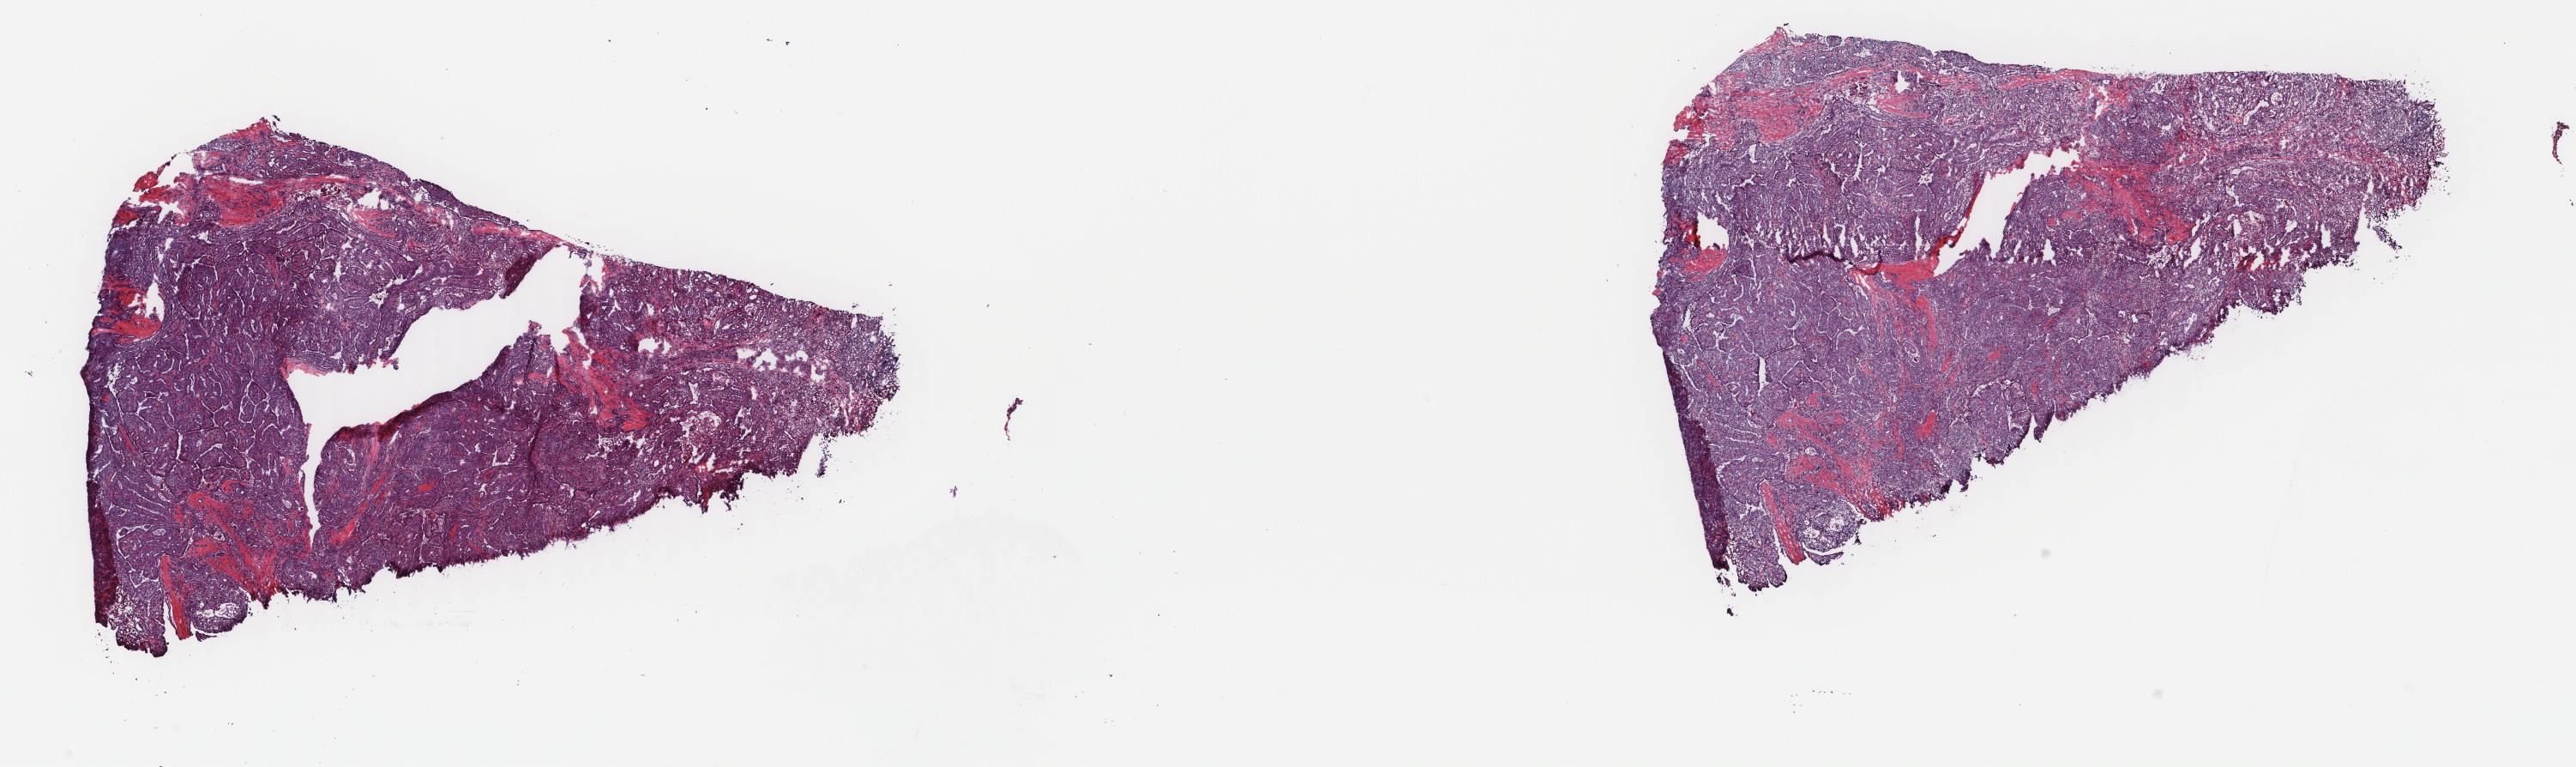
Digitized H&E-stained tissue section (whole slide), whole scanned area (about 23.8 x 7.1 mm) shown as a low-resolution overview, frozen section from the top of the tissue portion, primary tumour sample from the thyroid. Female, age 21 years at initial diagnosis. Pathologist review of this section (percent, as recorded): tumour cells 85%, tumour nuclei 65%, normal cells 5%, stromal cells 10%, necrosis 0%. Inflammatory infiltration, as recorded: lymphocyte infiltration 0%, monocyte infiltration 0%, neutrophil infiltration 0%.
Histologic diagnosis: Papillary adenocarcinoma, NOS (thyroid gland). AJCC pathologic stage: I (6th edition).